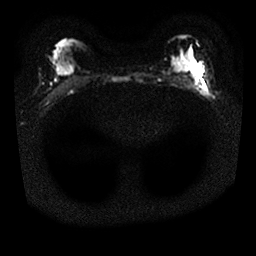
Breast MRI, one axial slice. Position 17 of 25 along the scan axis. Diffusion-weighted series; image 2 of 4 stored at this slice position (different b-values; order by instance number). 1.5 T. 4 mm slice thickness. 256 × 256 image matrix, field of view 310 × 310 mm. Female patient.
Outlined on this slice (expert manual segmentation):
- tumour on diffusion-weighted imaging: bounding box <198,69,205,90> (left, top, right, bottom; pixels)